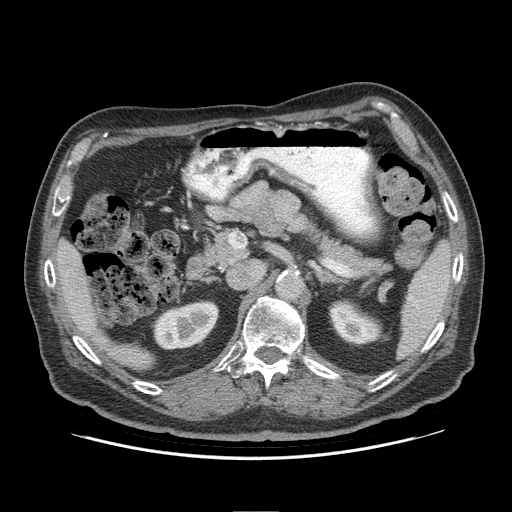
Contrast-enhanced abdominal CT (liver protocol), one axial slice; slice 49 of 95 in the series (ordered by position); reconstruction kernel STANDARD; 140 kVp; soft-tissue window (W 400 / L 40 HU); 512 × 512 image matrix. From the clinical record (not read from this slice): diagnosis: hepatocellular carcinoma (patient treated with transarterial chemoembolisation; whether this scan precedes or follows treatment is not stated here); TNM stage (as recorded): Stage-IVB; Child-Pugh class: A.
Annotated regions visible in this slice (semi-automatic segmentation, software-assisted and operator-edited):
- liver parenchyma outside the tumour (the mass and vessels are separate outlines, so this box may not span the whole liver): bounding box <54,239,106,344> (left, top, right, bottom; pixels)